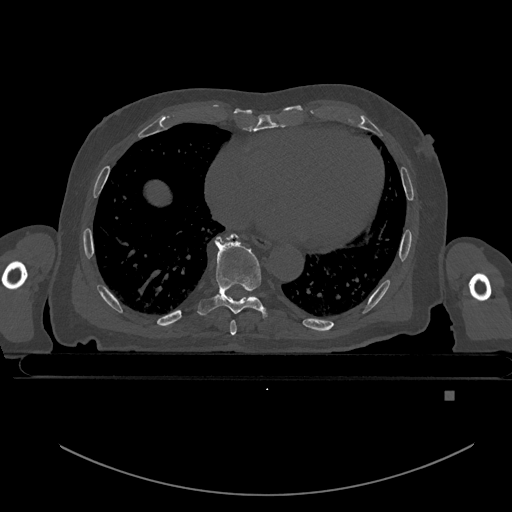
CT including the spine, one axial slice. Position 201 of 969 along the scan axis. Bone window (W 1800 / L 400 HU). 512 × 512 image matrix. Male patient, age 82 years. From the clinical record (not read from this slice): primary cancer: prostate.
Outlined on this slice (semi-automatic segmentation, software-assisted and operator-edited):
- T7 vertebra: bounding box [x1, y1, x2, y2] px = [230, 320, 236, 335]
- T8 vertebra: [197, 235, 271, 320]
- T9 vertebra: [230, 235, 234, 239]